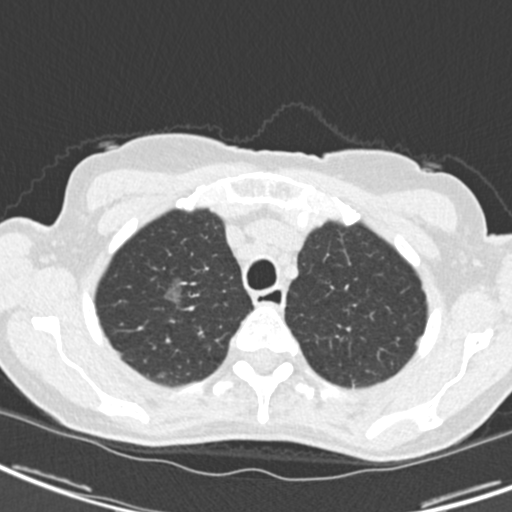
Low-dose screening chest CT, one axial slice; slice 164 of 189 in the series (ordered by position); reconstruction kernel B30f; lung window (W 1500 / L -600 HU); 2 mm slice thickness; 512 × 512 image matrix, field of view 279 × 279 mm.
Outlined on this slice (outlined manually by an expert reader):
- lesion 1 (tumor, upper lobe of right lung): bounding box (x1, y1, x2, y2) in pixels: (165, 279, 183, 304)